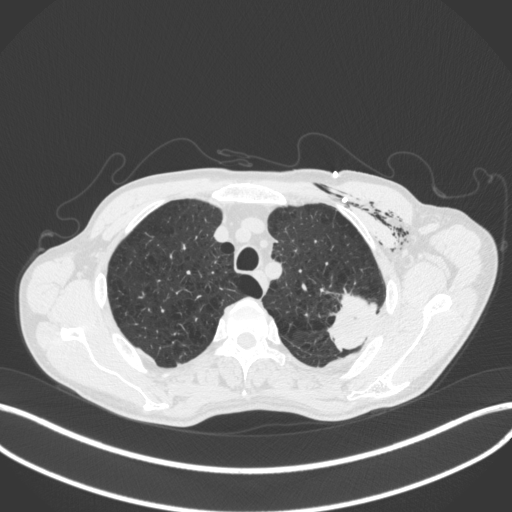
Chest CT, one axial slice; position 334 of 416 along the scan axis; lung window (W 1500 / L -600 HU); 1 mm slice thickness; 512 × 512 image matrix. Patient: male, 58 years. Case-level facts recorded for this patient, not image findings: clinical TNM (as recorded): T3 N0 M0.
Annotated regions visible in this slice (bounding box drawn by a radiologist):
- lung tumour (recorded histology: adenocarcinoma): box from (x=321, y=287) to (x=383, y=353) px